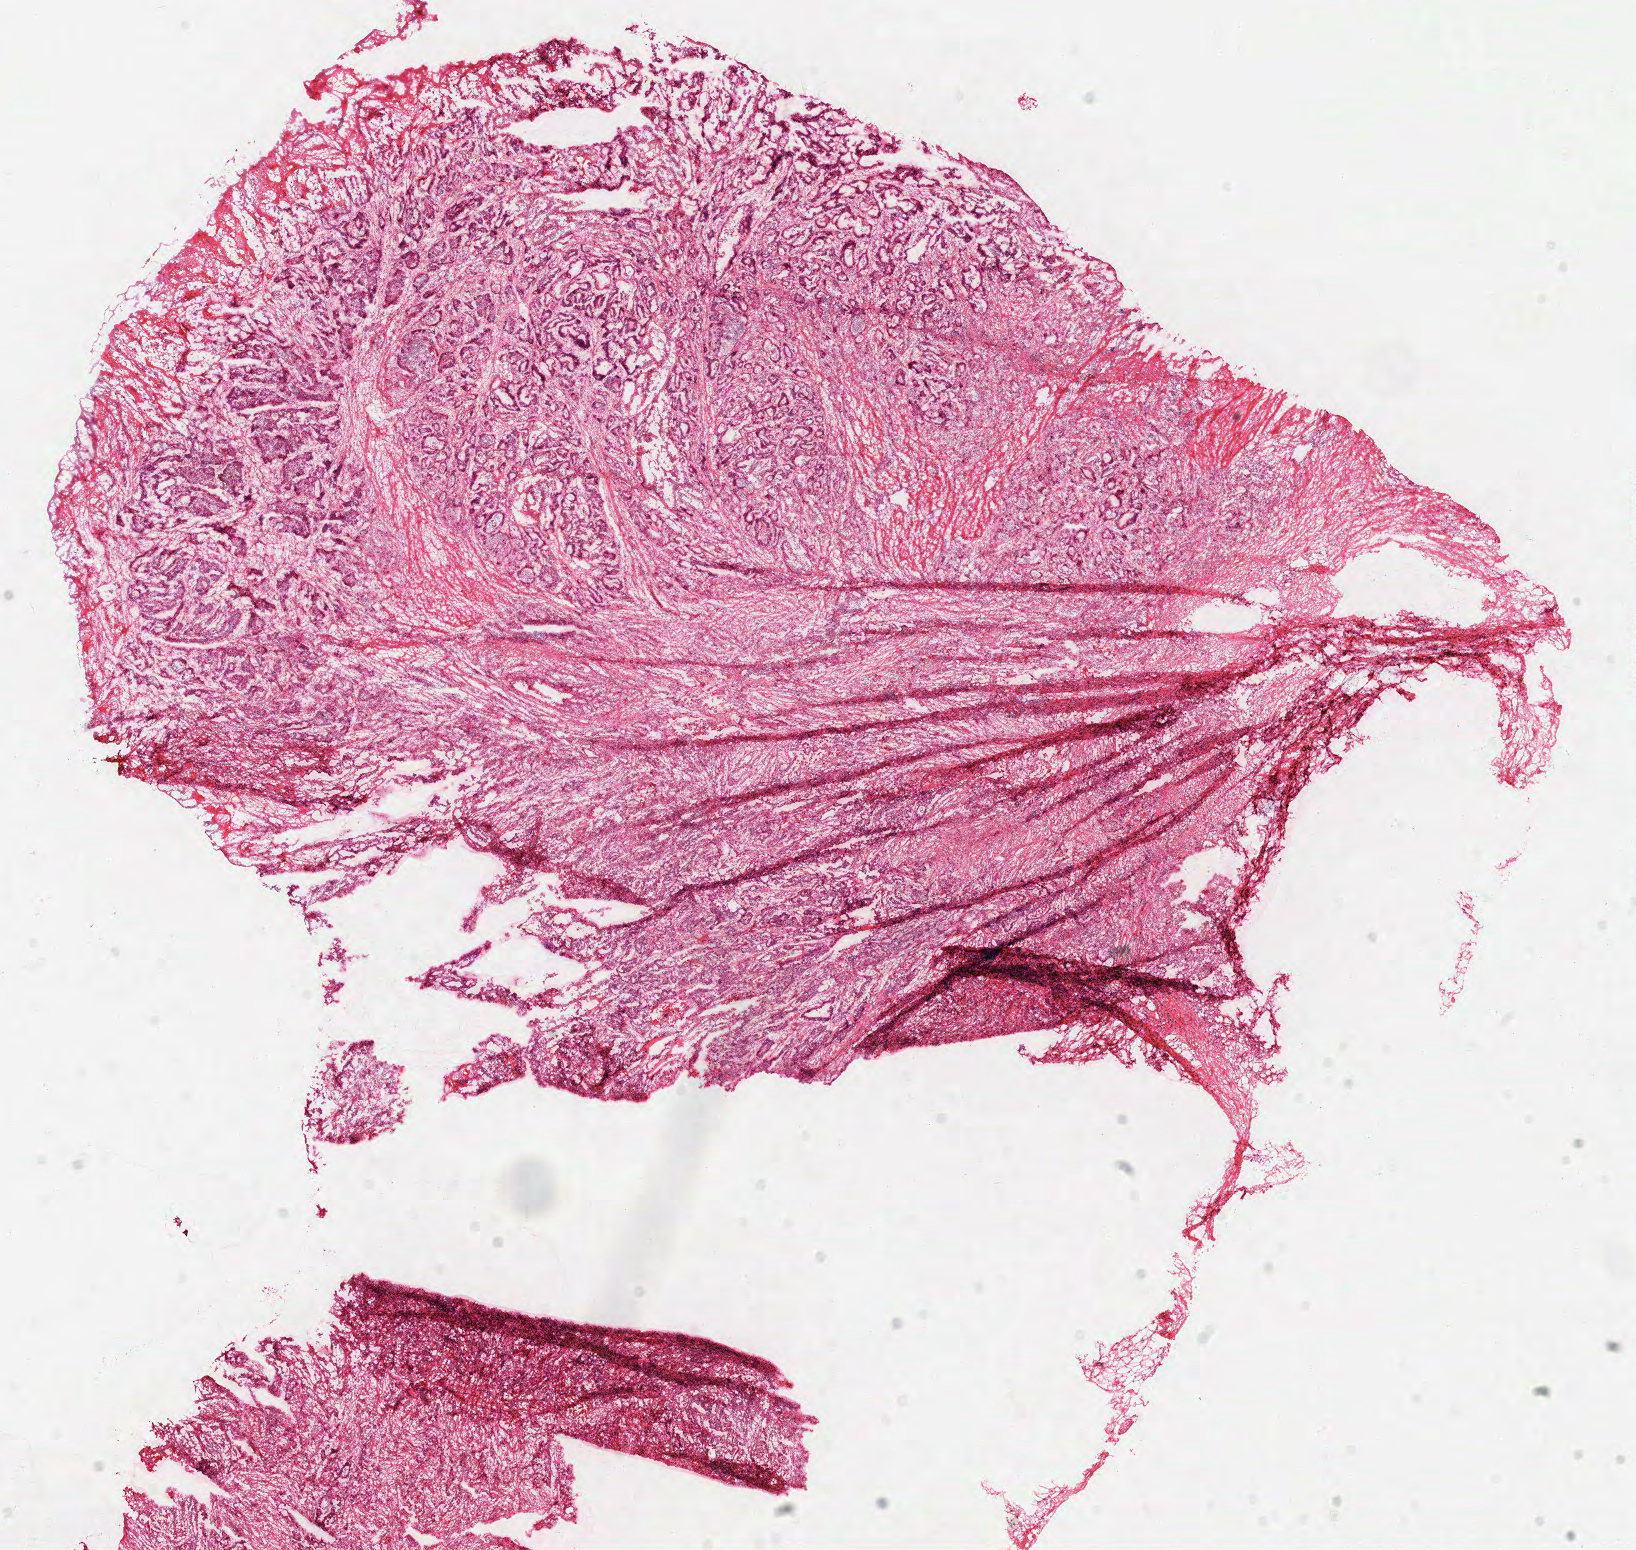
Digitized H&E tissue section (whole slide) — shown as a low-resolution overview of the whole scanned area (about 12.9 x 12.2 mm, from a 40x scan). Frozen section. Primary tumour sample from the colon. Patient: male, age at initial diagnosis 64 years. Pathologist review of this section (percent, as recorded): tumour cells 65%, tumour nuclei 75%, normal cells 0%, stromal cells 30%, necrosis 5%.
- histologic diagnosis: Adenocarcinoma, NOS
- AJCC pathologic stage: IIA
- TNM: T3 N0 M0